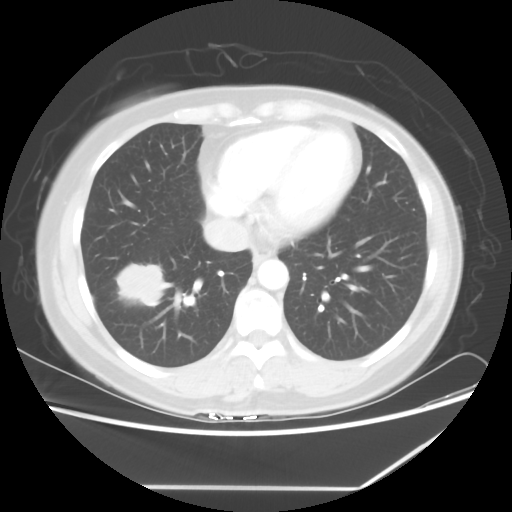
Chest CT, one axial slice; position 22 of 60 along the scan axis; reconstruction kernel STANDARD; 100 kVp; lung window (W 1500 / L -600 HU); 512 × 512 image matrix. Female patient, age 42 years. From the clinical record (not read from this slice): clinical TNM (as recorded): T2 N1 M0.
Structures marked on this image (rectangle marked by the reading radiologist):
- lung tumour (recorded histology: adenocarcinoma): box from (x=109, y=255) to (x=169, y=312) px